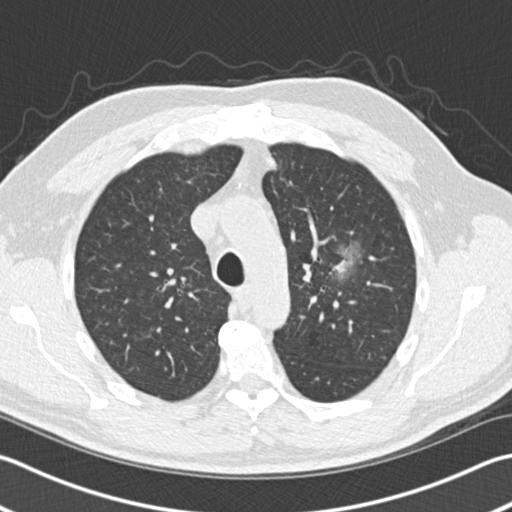
Axial slice from a low-dose chest CT screening exam; third annual screen; lung window (W 1500 / L -600 HU); 2 mm slice thickness; slice 41 of 153 in the series; 512 × 512 image matrix. Male participant, aged 65 years at enrolment. Former smoker at enrolment.
- Expert reader's lesion annotation, bounding box <306,241,370,306> (left, top, right, bottom; pixels).
- The screening reader recorded 4 non-calcified nodules or masses ≥4 mm on this exam; which of them this box marks is not recorded.
- Official screen result: positive, other.
- Later outcome: lung cancer diagnosed 196 days after this screen — acinar cell carcinoma, left upper lobe, stage IA (AJCC 6th edition), 25 mm at pathology.